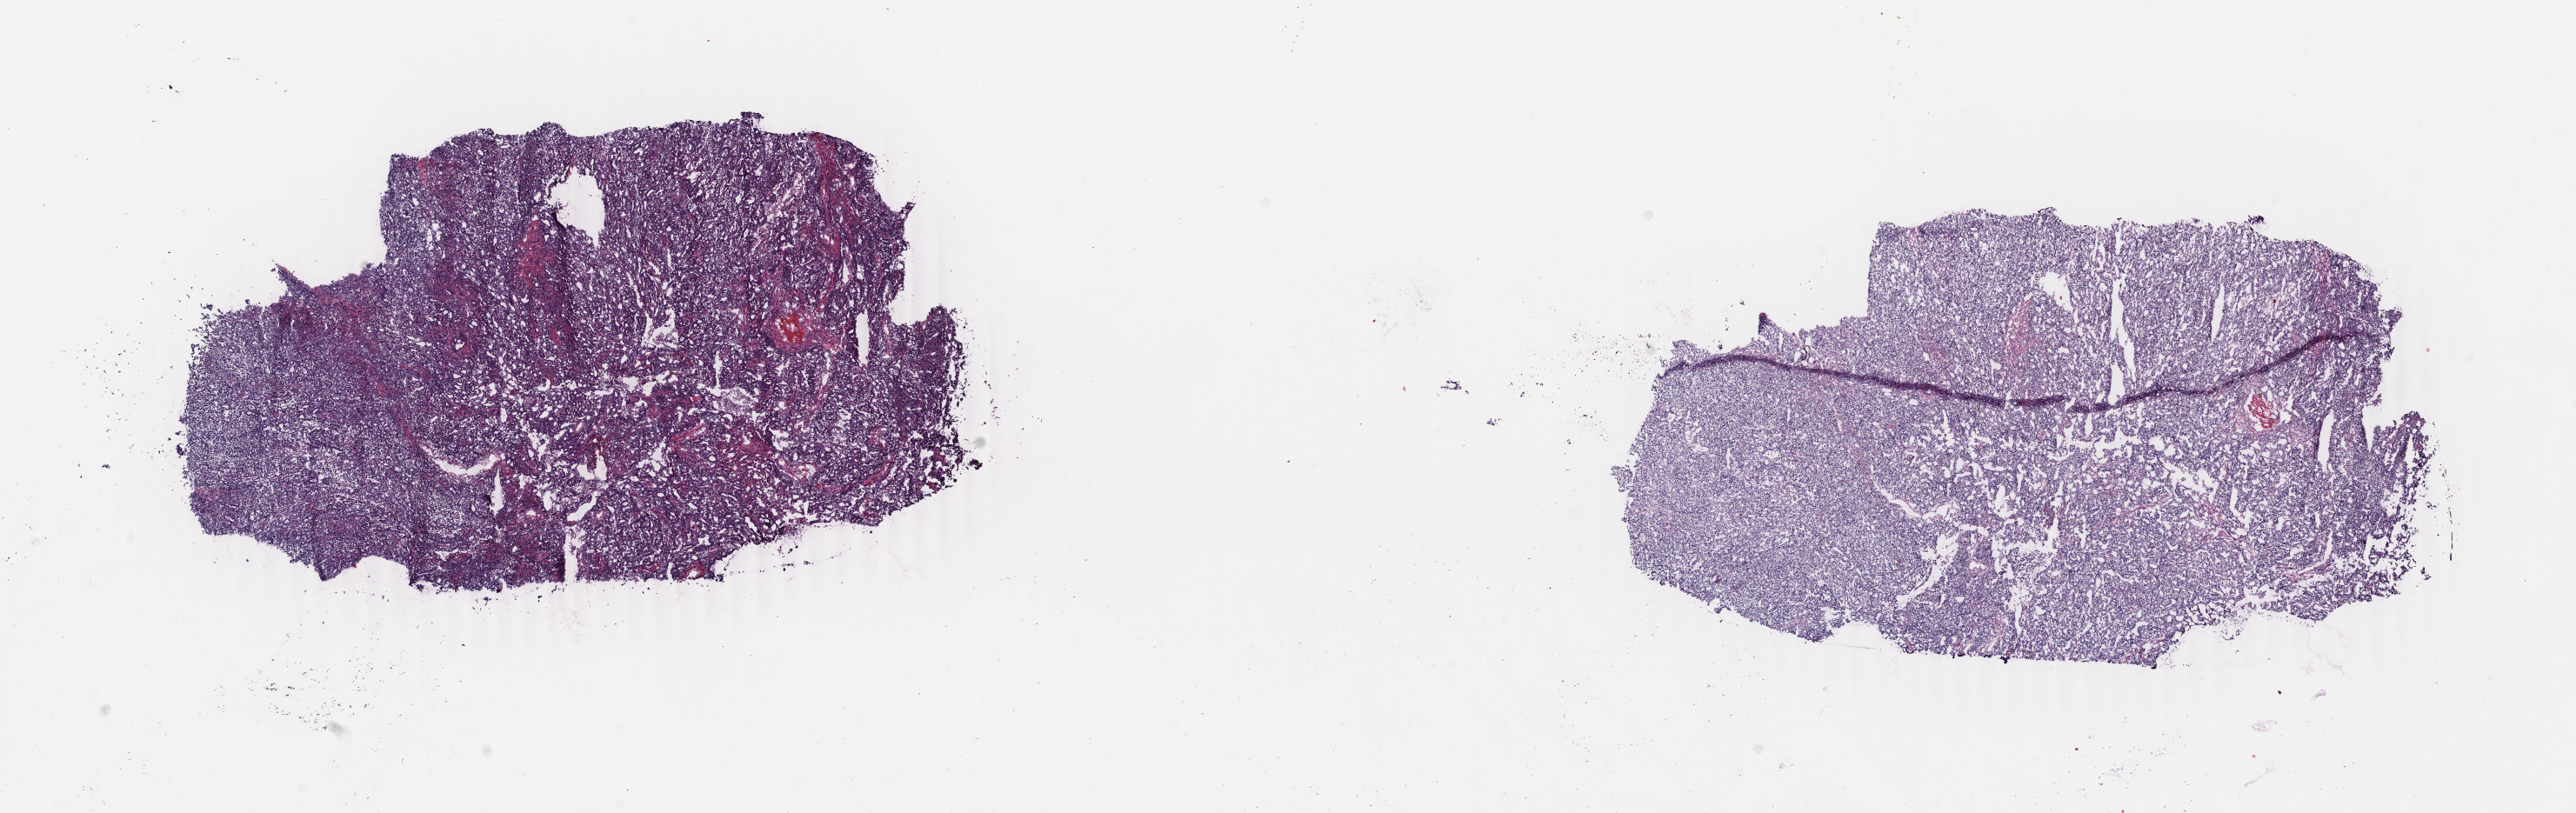
Digitized H&E-stained tissue section (whole slide), shown as a low-resolution overview of the whole scanned area (about 23.6 x 7.4 mm, from a 40x scan); frozen section; primary tumour sample from the uterus. Female patient; age at initial diagnosis 58 years. Histologic grade: G3 (poorly differentiated). Pathologist review of this section (percent, as recorded): tumour cells 90%, tumour nuclei 90%, normal cells 0%, stromal cells 5%, necrosis 5%. Infiltration values recorded for this section: lymphocyte infiltration 40%, monocyte infiltration 20%, neutrophil infiltration 30%.
Histologic diagnosis: Endometrioid adenocarcinoma, NOS. Lymph nodes positive (case pathology): 2 of 14 examined. FIGO stage: IVB.